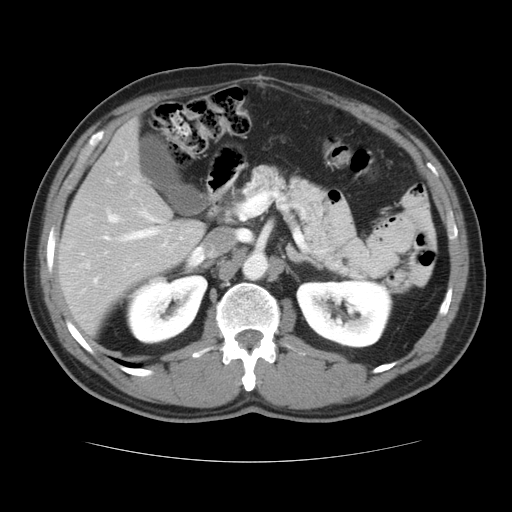
Contrast-enhanced abdominal CT, one axial slice. Position 19 of 37 along the scan axis. Reconstruction kernel STANDARD. 120 kVp. Intravenous contrast given. Soft-tissue window (W 400 / L 40 HU). 5 mm slice thickness. 512 × 512 image matrix. Male patient, age 66 years. Case-level facts recorded for this patient, not image findings: diagnosis: colorectal cancer liver metastases, imaged before liver resection; multiple liver metastases: yes; largest metastasis: 1.6 cm; disease in both lobes: yes.
Outlined on this slice (outlined manually by an expert reader):
- hepatic veins: bounding box (x1, y1, x2, y2) in pixels: (107, 173, 204, 267)
- liver: (60, 121, 205, 335)
- planned liver remnant (the part of the liver to remain after resection): (60, 202, 205, 335)
- portal vein (with intrahepatic branches): (94, 213, 158, 283)